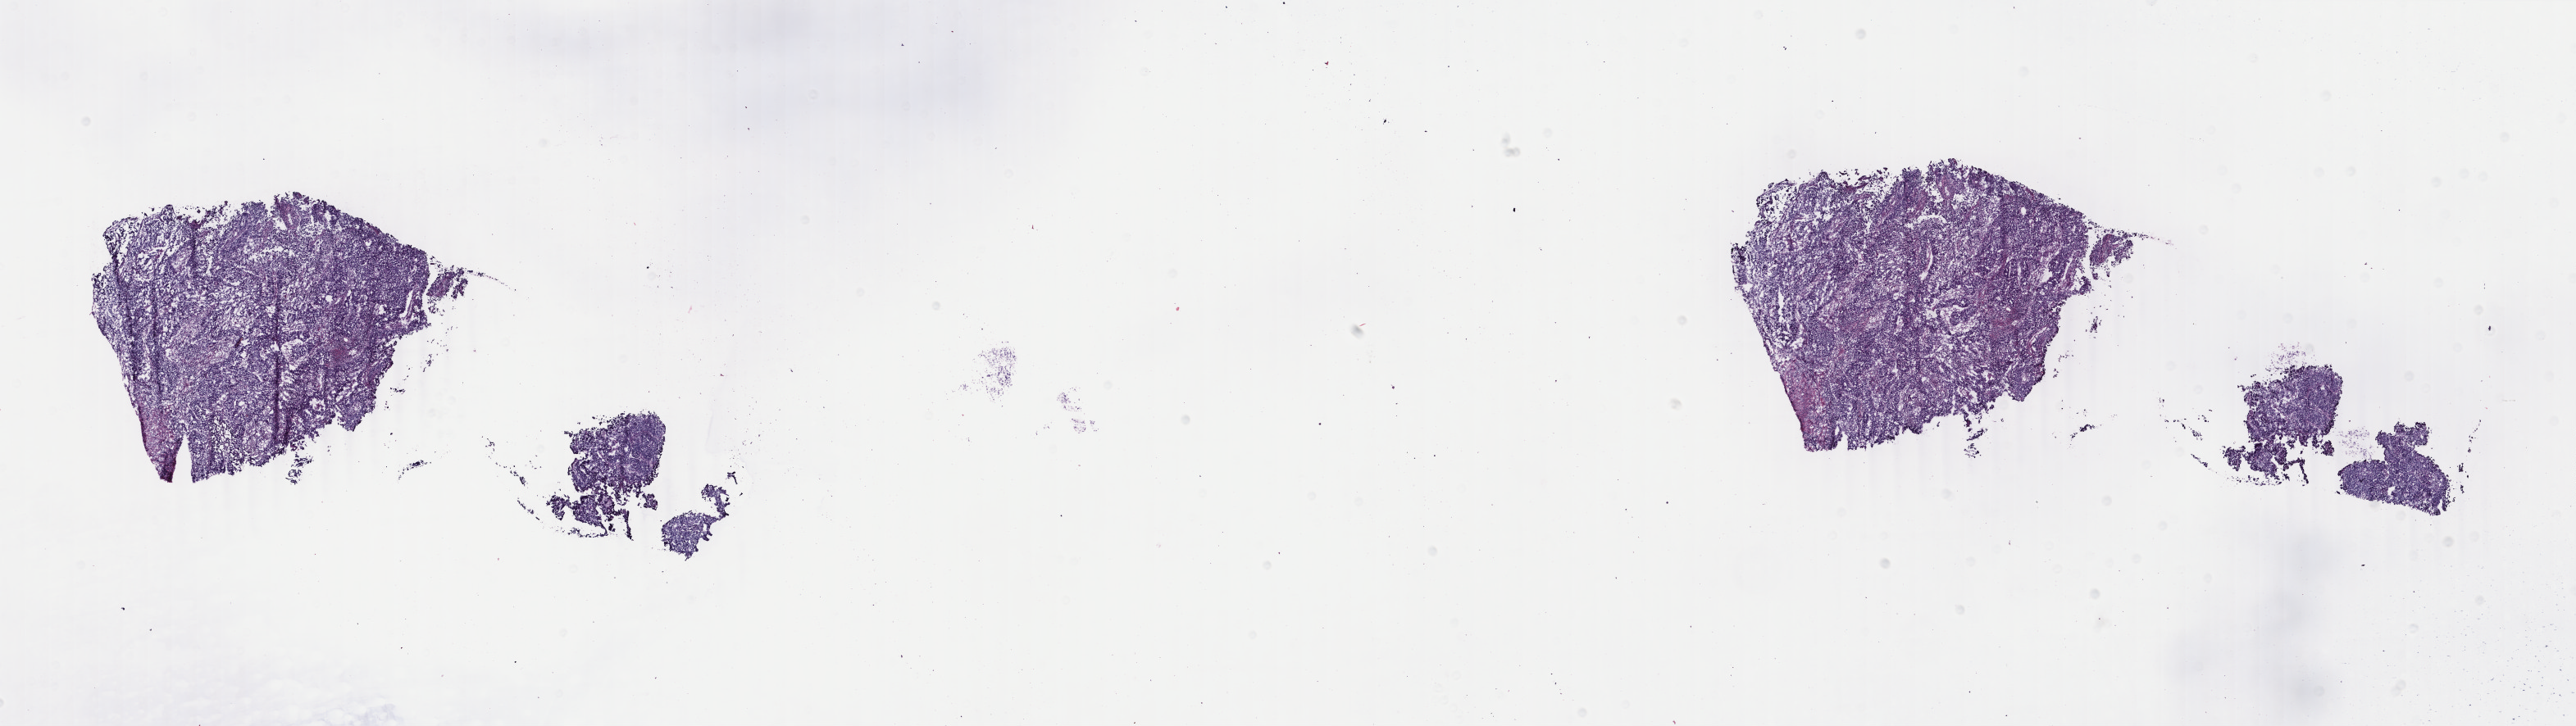
Digitized H&E tissue section (whole slide), whole scanned area (about 25.0 x 7.0 mm, slide scanned at 40x) shown as a low-resolution overview, frozen section, primary tumour sample from the uterus. Female, age 62 years at initial diagnosis.
Pathologic diagnosis: Endometrioid adenocarcinoma, NOS (endometrium).